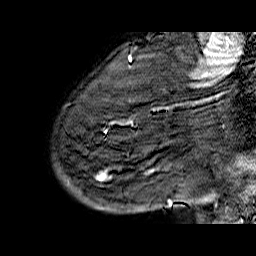
Breast MRI (dynamic contrast-enhanced), one sagittal slice; position 51 of 60 along the scan axis; dynamic contrast-enhanced series, time point 2 of 6 at this slice position (early post-contrast); 1.5 T; TE 6.5 ms, TR 32.9 ms; 4 mm slice thickness; 256 × 256 image matrix. Female patient. From the clinical record (not read from this slice): setting: breast cancer imaged before/during neoadjuvant chemotherapy; receptor status: HR-positive, HER2-negative.
Outlined on this slice (semi-automatic segmentation, software-assisted and operator-edited):
- analysis volume of interest (the breast-tissue region the enhancement analysis was run in; not a lesion): bounding box <53,74,176,210> (left, top, right, bottom; pixels)
- tumour enhancement mask (voxels above the 100 % enhancement threshold inside the analysis volume of interest): <105,172,172,206>